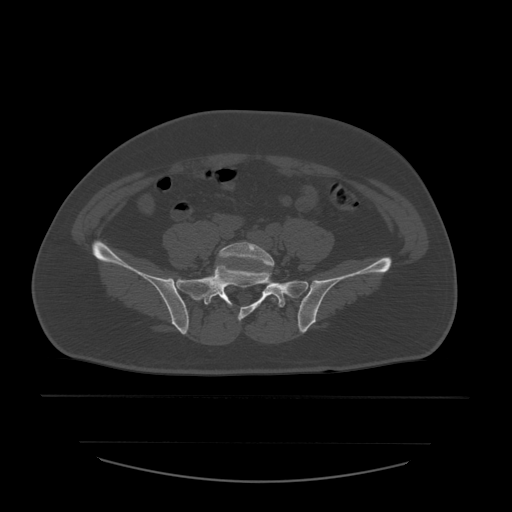
CT including the spine, one axial slice. Slice 106 of 532 in the series (ordered by position). 120 kVp. Bone window (W 1800 / L 400 HU). 1.25 mm slice thickness. 512 × 512 image matrix, field of view 441 × 441 mm. Patient age 44 years. From the clinical record (not read from this slice): primary cancer: soft tissue sarcoma.
Structures marked on this image (semi-automatic segmentation, software-assisted and operator-edited):
- L5 vertebra: bounding box <218,242,276,302> (left, top, right, bottom; pixels)